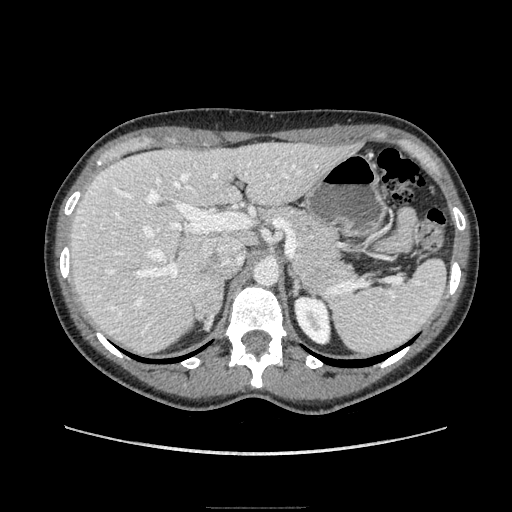
Contrast-enhanced abdominal CT, one axial slice. Position 119 of 193 along the scan axis. Soft-tissue window (W 400 / L 40 HU). 1.25 mm slice thickness. 512 × 512 image matrix, field of view 380 × 380 mm. Female patient. From the clinical record (not read from this slice): diagnosis: adrenocortical carcinoma; tumour side: right adrenal; tumour size at pathology: 3 cm.
Outlined on this slice (semi-automatically segmented with operator editing):
- mass: bounding box (x1, y1, x2, y2) in pixels: (196, 277, 223, 326)